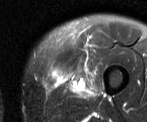
MRI of an extremity soft-tissue mass, one axial slice. Slice 9 of 52 in the series (ordered by position). T2-weighted fat-saturated. MR volume resampled by the dataset authors to the PET/CT grid (not the native acquisition matrix). 3.27 mm slice thickness. 147 × 122 image matrix, field of view 144 × 119 mm. Male patient. From the clinical record (not read from this slice): histological type: pleiomorphic liposarcoma; grade: high; site of the primary tumour: left thigh.
Structures marked on this image (expert contour drawn on MRI and transferred to this co-registered scan by the dataset authors):
- gross tumour volume including surrounding oedema: box from (x=62, y=64) to (x=95, y=97) px